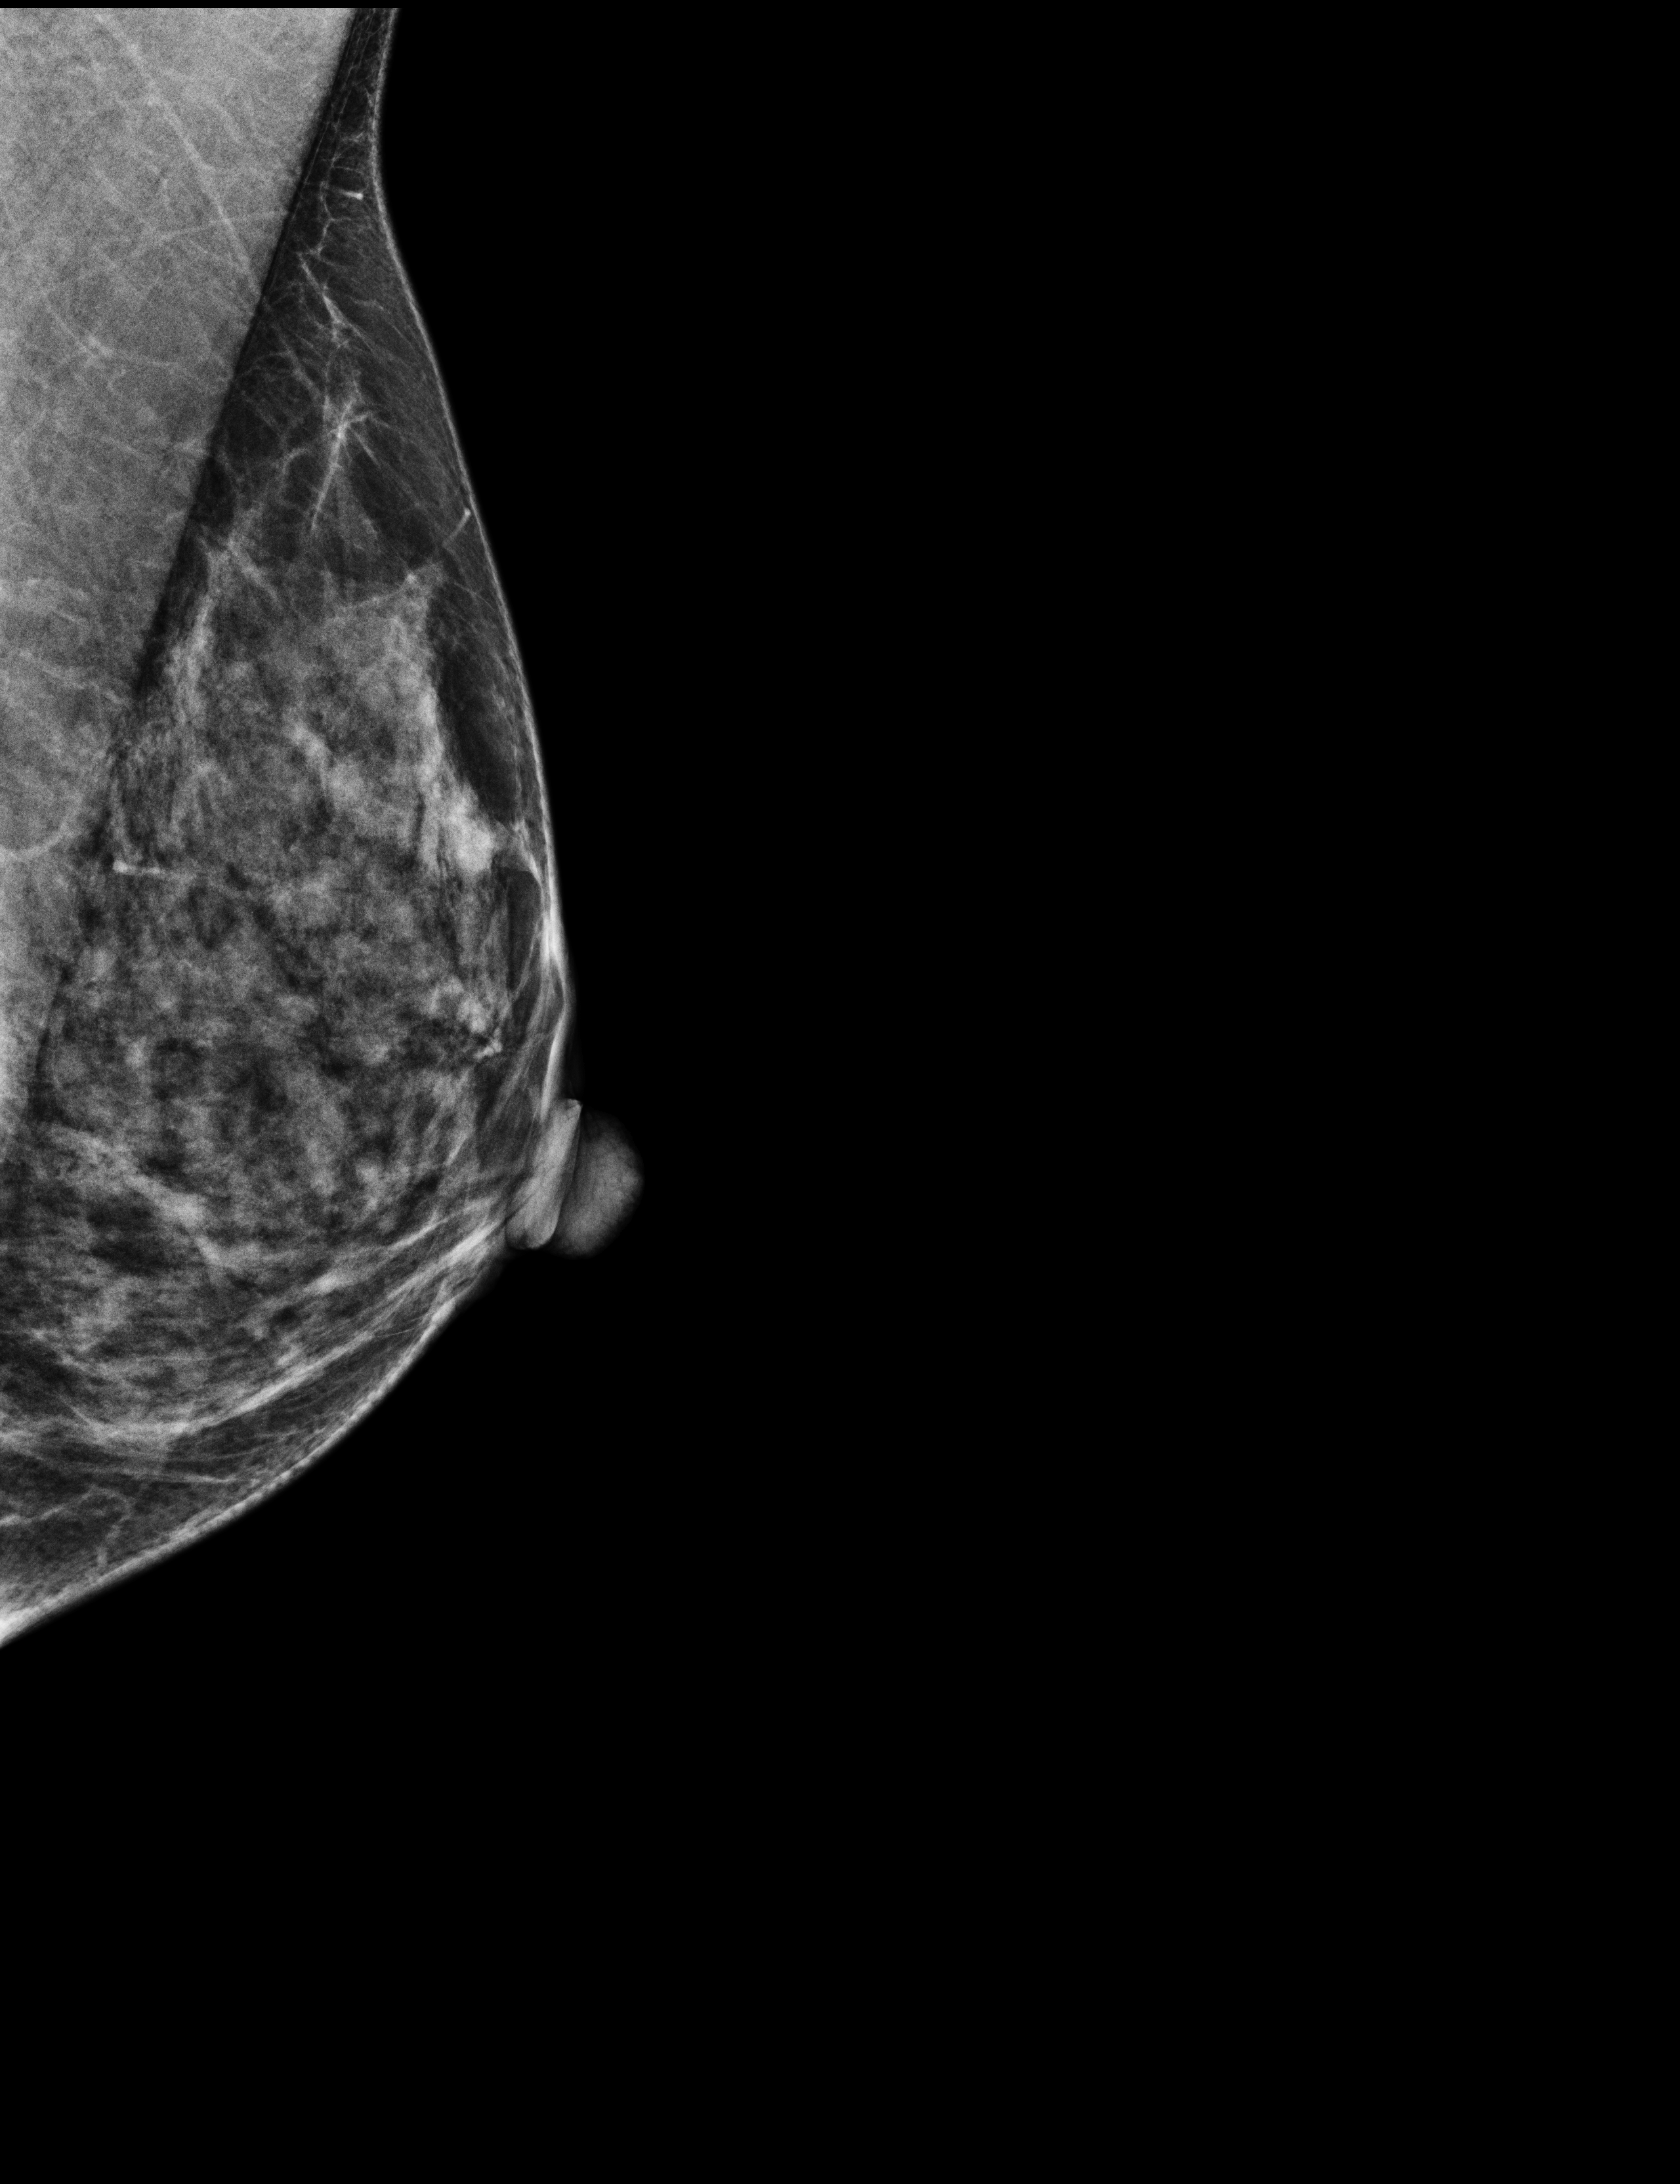
Full-field digital mammogram (FFDM), left breast, mediolateral oblique (MLO) view, annual screening mammography examination, system: Selenia Dimensions. Patient: female, 42 years.
BI-RADS breast density category at the screening exam (both breasts, scale 1–4): 3. Final BI-RADS category for the screening round (tomosynthesis exam, both breasts): category 1. Recall: no recall after this screen.